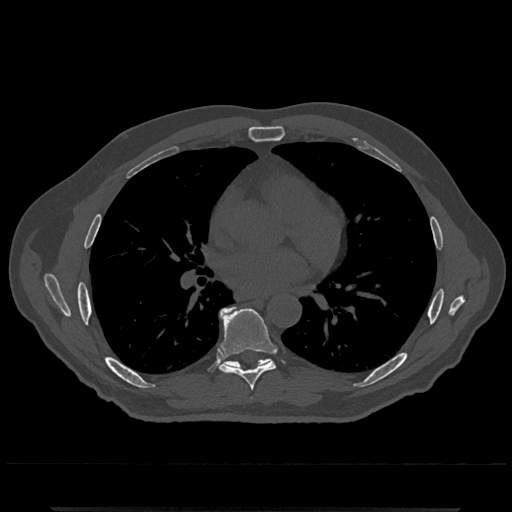
CT including the spine, one axial slice. Position 709 of 797 along the scan axis. 120 kVp. Bone window (W 1800 / L 400 HU). 0.5 mm slice thickness. 512 × 512 image matrix, field of view 393 × 393 mm. Male patient, age 67 years. From the clinical record (not read from this slice): primary cancer: prostate.
Structures marked on this image (semi-automatic segmentation, software-assisted and operator-edited):
- T7 vertebra: bounding box <219,308,276,391> (left, top, right, bottom; pixels)
- T8 vertebra: <219,306,271,368>